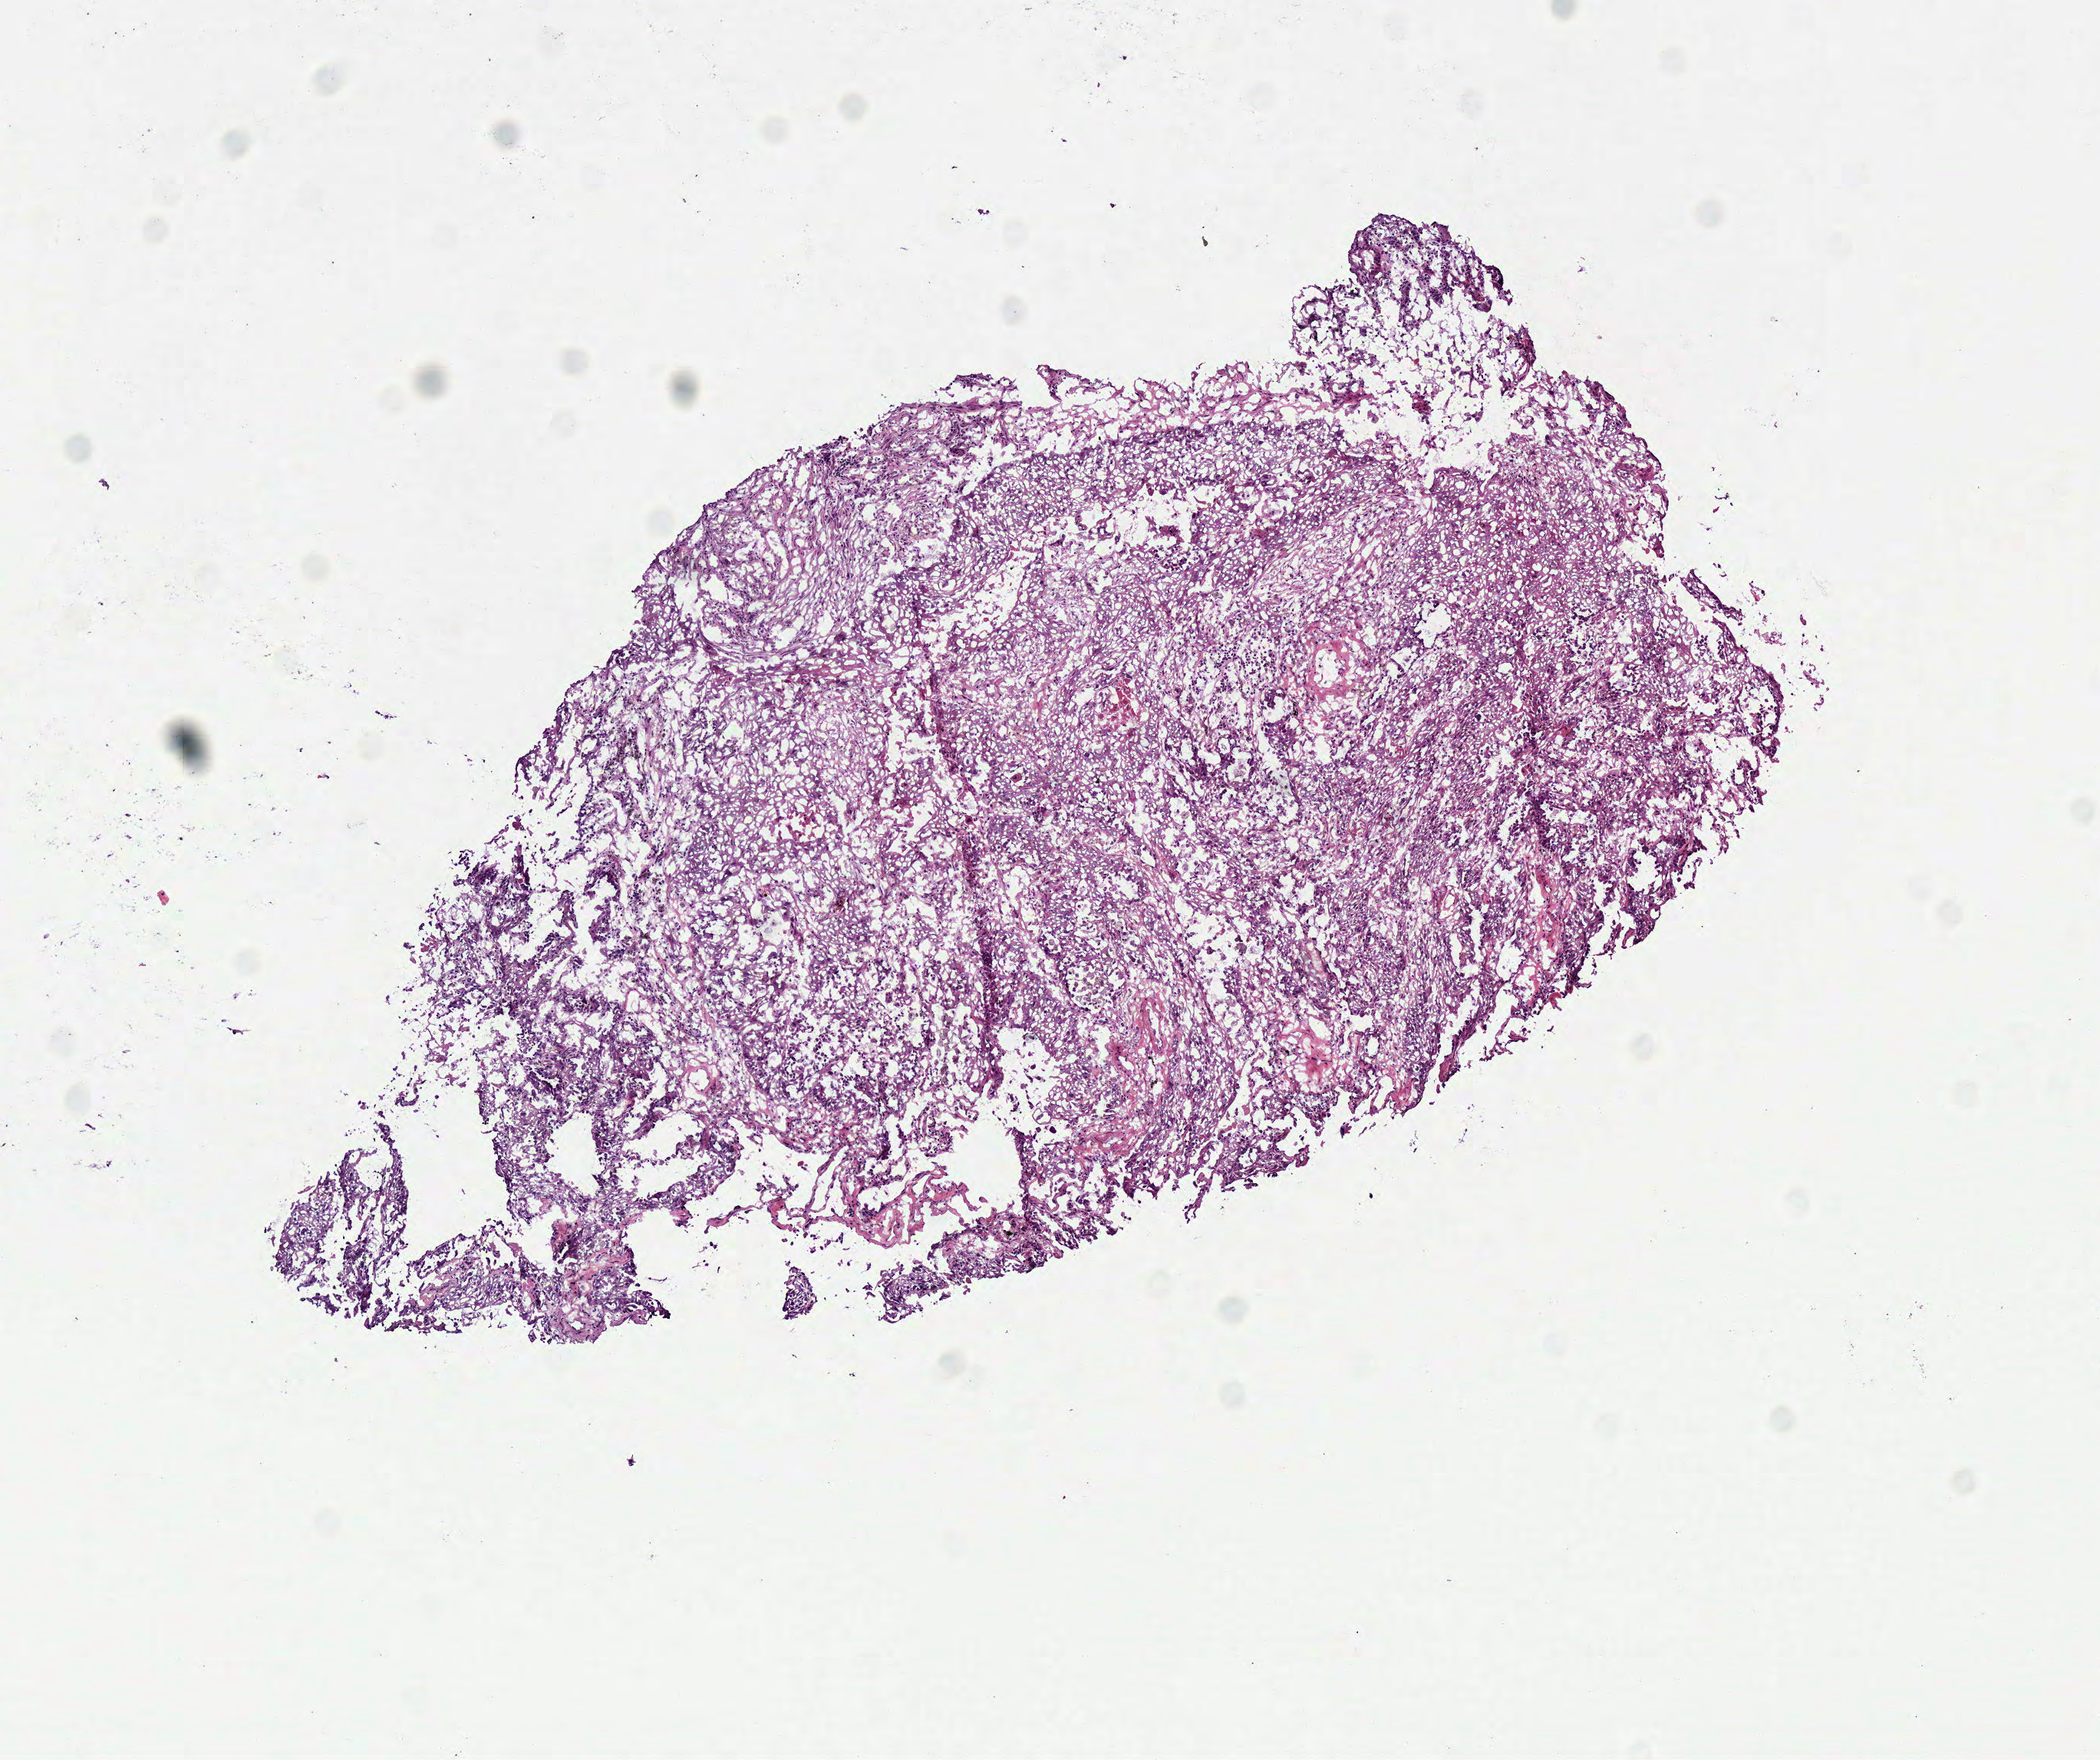
Whole-slide histology image, H&E-stained, shown as a low-resolution overview of the whole scanned area (about 5.4 x 4.5 mm). Frozen section. Sample: primary tumour, lung. Male patient; age at initial diagnosis 69 years. Slide review estimates, as recorded: tumour cells 87%, tumour nuclei 85%, normal cells 0%, stromal cells 10%, necrosis 3%. Inflammatory infiltration, as recorded: lymphocyte infiltration 5%, monocyte infiltration 0%, neutrophil infiltration 0%.
TNM: T1b N0 M0. AJCC pathologic stage: IA (7th edition). Histologic diagnosis: Squamous cell carcinoma, NOS (upper lobe, lung). Laterality: right.